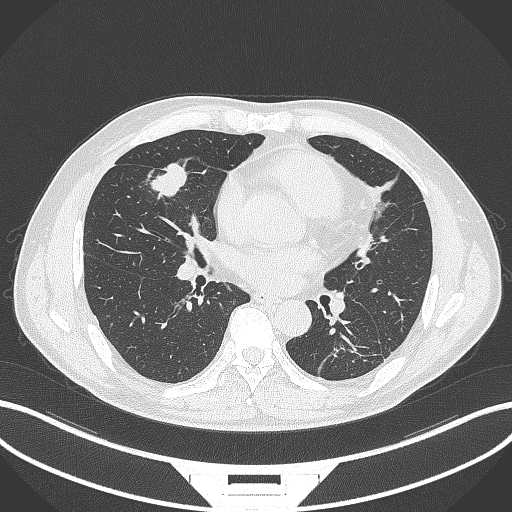
Chest CT, one axial slice. Position 144 of 399 along the scan axis. Reconstruction kernel B70f. Lung window (W 1500 / L -600 HU). 512 × 512 image matrix, field of view 400 × 400 mm. Male patient, age 59 years. Case-level facts recorded for this patient, not image findings: clinical TNM (as recorded): T2a N1 M0.
Structures marked on this image (rectangle marked by the reading radiologist):
- lung tumour (recorded histology: adenocarcinoma): bounding box [x1, y1, x2, y2] px = [148, 161, 197, 200]